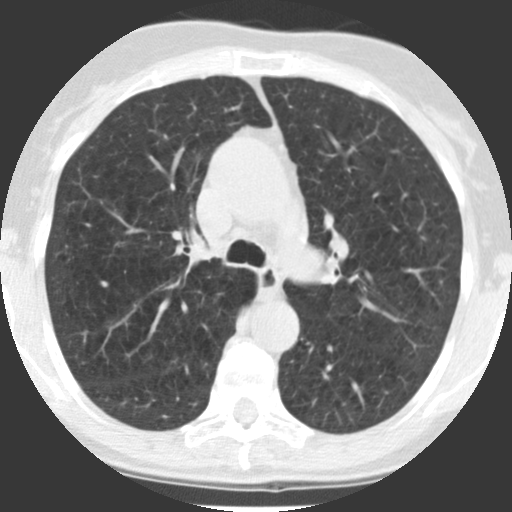
Low-dose screening chest CT, axial slice, first (baseline) screen, lung window (W 1500 / L -600 HU), slice 73 of 238 in the series. Female, age 71 years at enrolment.
Expert-annotated lung lesion, bounding box (x1, y1, x2, y2) in pixels: (316, 335, 348, 363). Screening reader's record for this exam: no non-calcified nodule ≥4 mm recorded. Official screen result: negative screen, minor abnormalities not suspicious for lung cancer. Participant outcome: lung cancer diagnosed 802 days after this screen — squamous cell carcinoma, NOS, left lower lobe, poorly differentiated (G3), stage IB (AJCC 6th edition), 40 mm at pathology.